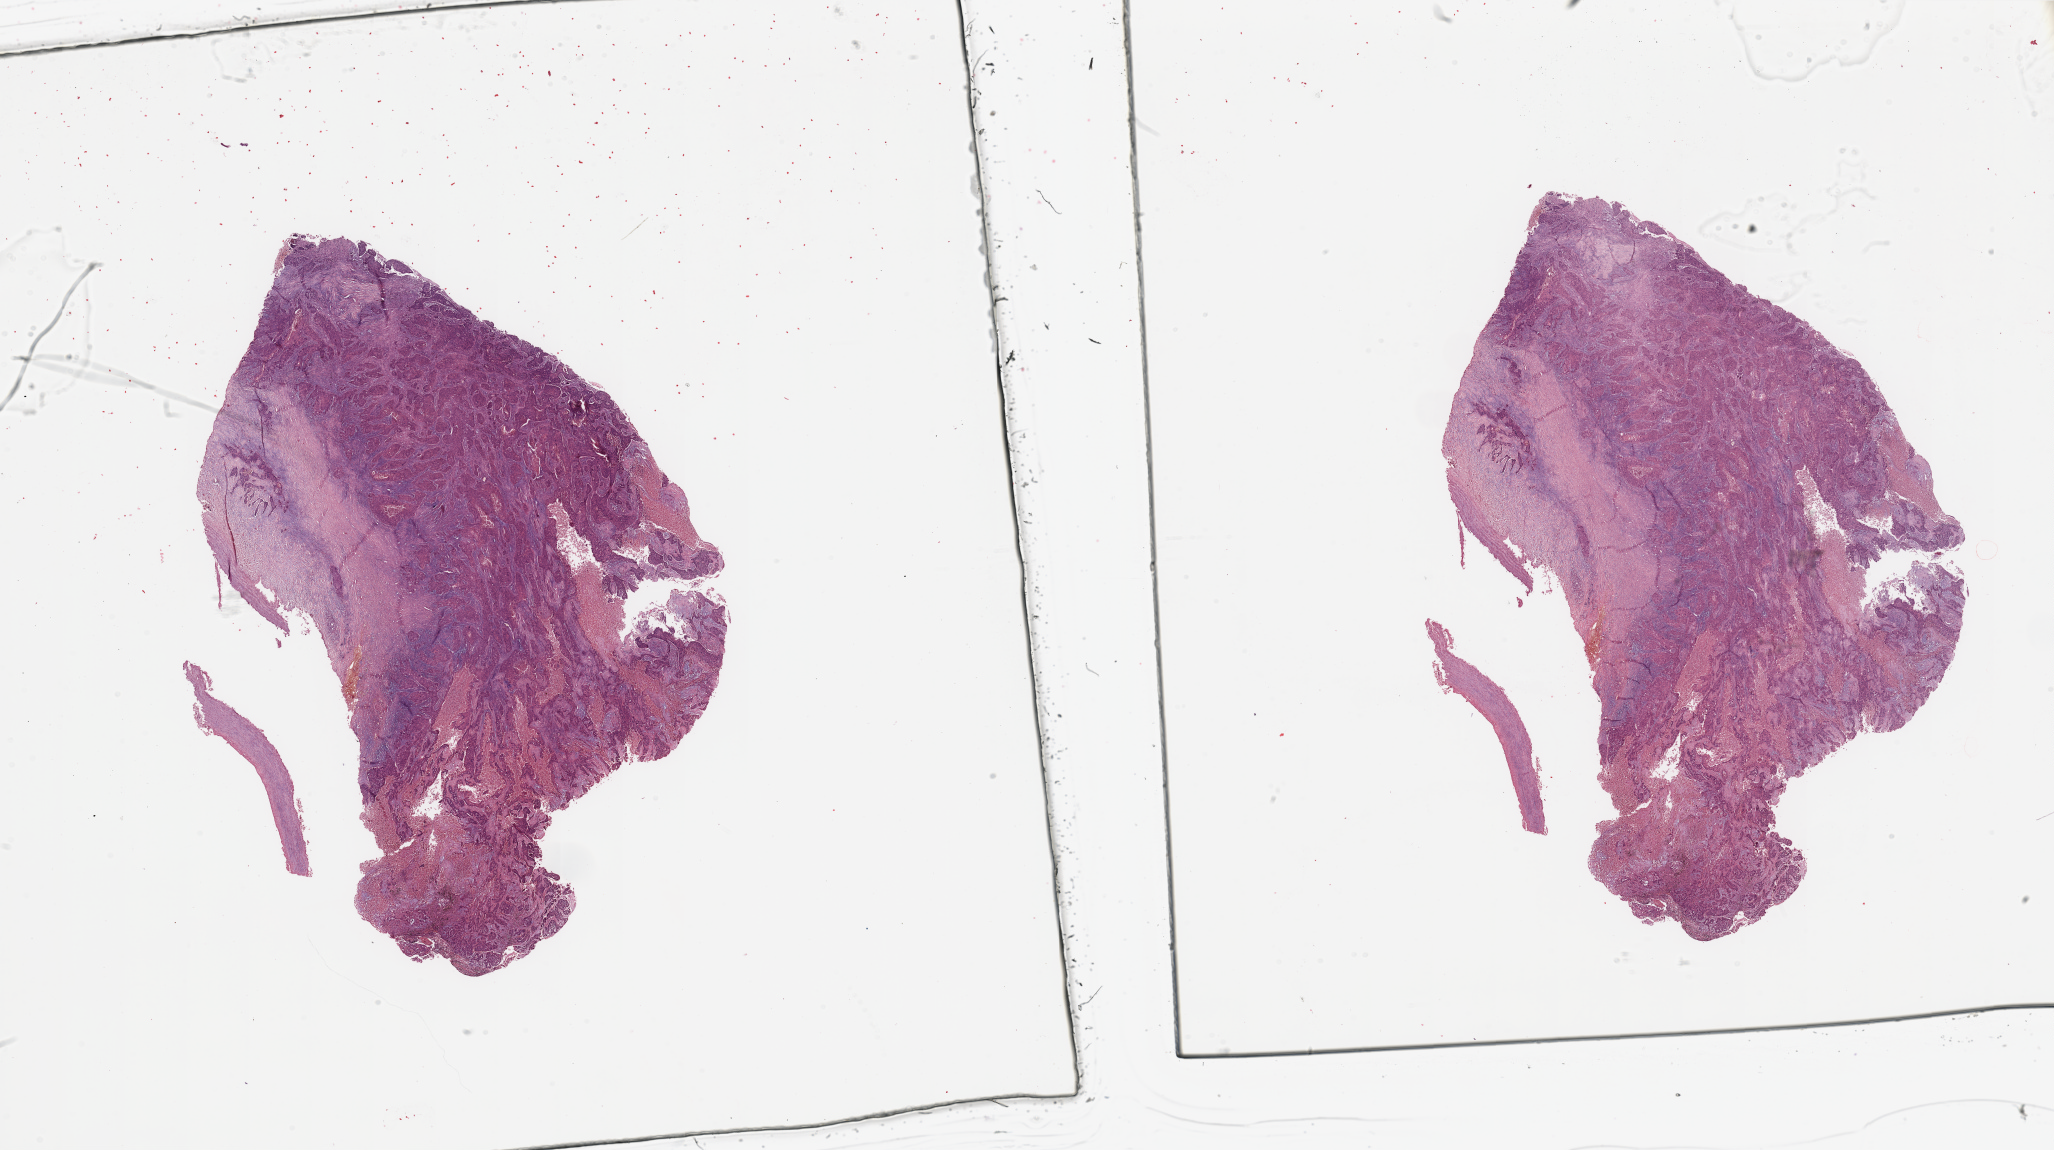
Whole-slide histology image, H&E-stained, low-resolution overview of the scanned area, about 32.5 x 18.2 mm (from a 20x scan); tumour tissue sample, lung. 64-year-old male patient. Histologic grade: G2 (moderately differentiated).
Diagnosis: Squamous cell carcinoma, NOS. AJCC pathologic stage: IIA.